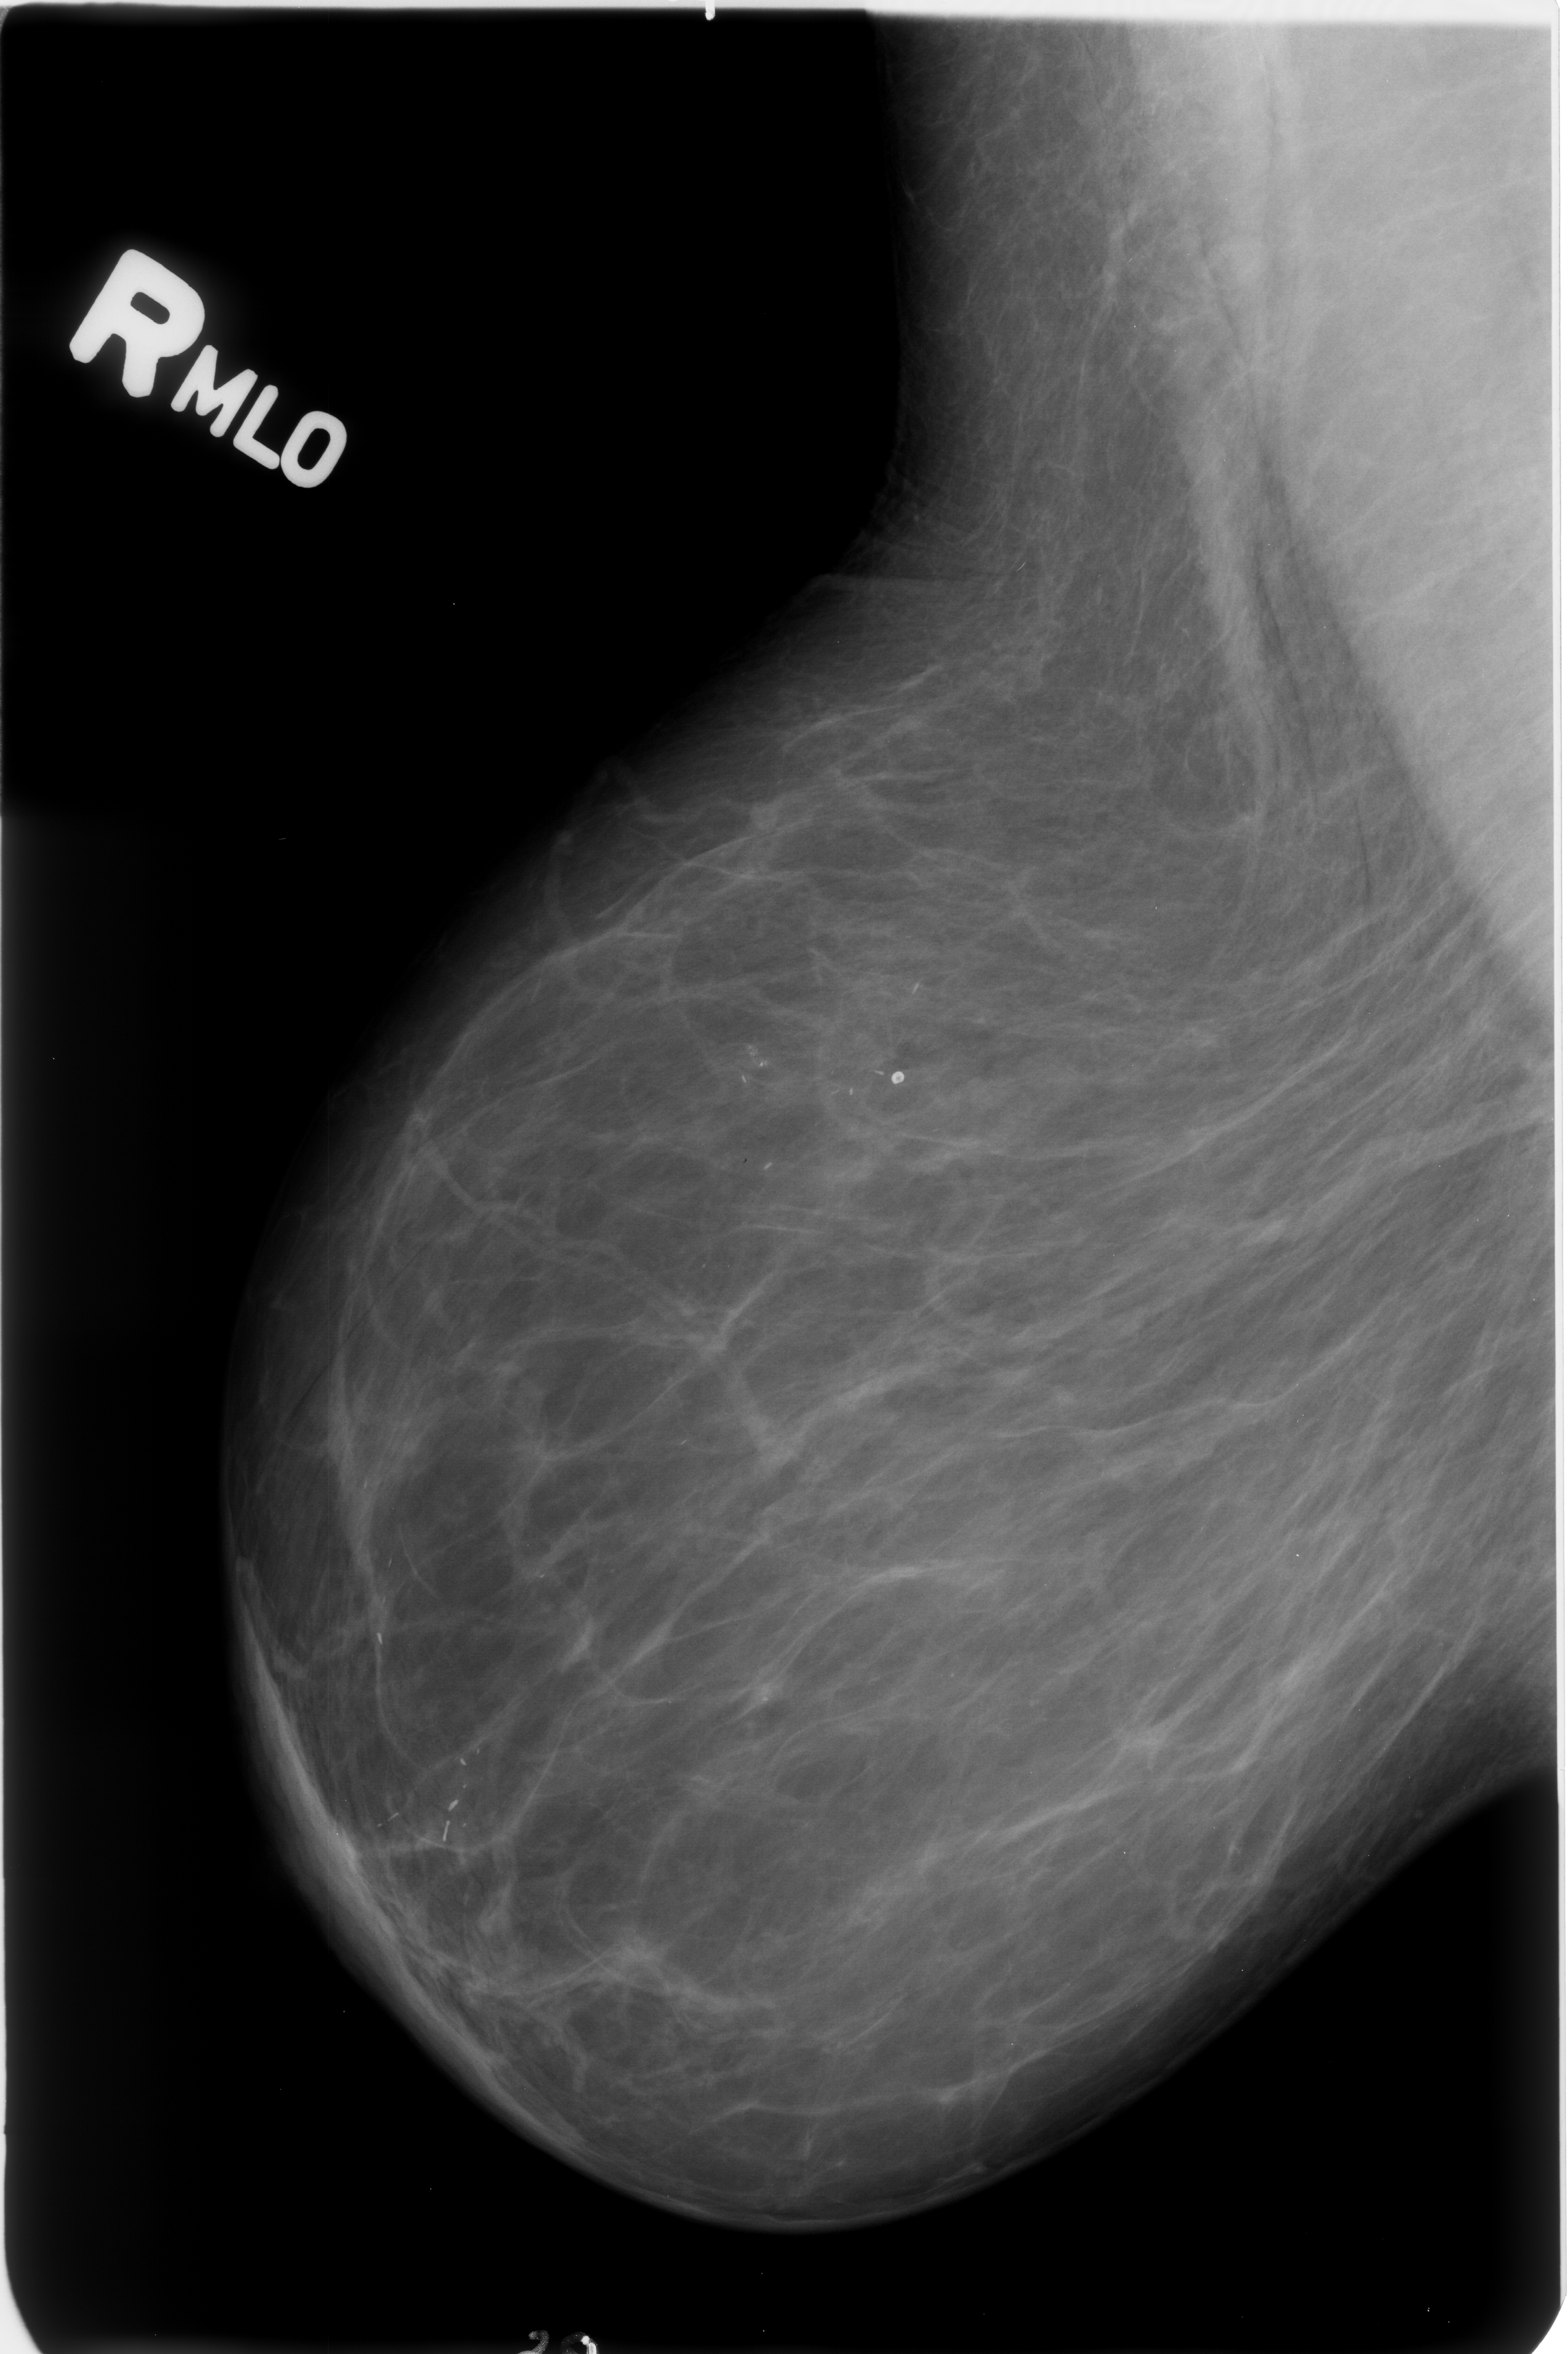
Digitized screen-film mammogram. Right breast. Mediolateral oblique (MLO) view. BI-RADS breast density category 1 (scale 1–4). 1568 × 2354 image matrix.
Expert-marked regions of interest on this film, with their recorded descriptors:
- Finding 1 of 5: calcifications, distribution regional; BI-RADS assessment category 2; subtlety rating 3 on a 1 (subtle) to 5 (obvious) scale; benign; no additional work-up was recommended (outcome (as recorded, no biopsy): benign without callback): bounding box [x1, y1, x2, y2] px = [349, 1547, 417, 1668]
- Finding 2 of 5: calcifications, distribution regional; BI-RADS assessment category 2; subtlety rating 3 on a 1 (subtle) to 5 (obvious) scale; benign; no additional work-up was recommended (outcome (as recorded, no biopsy): benign without callback): [358, 1802, 388, 1836]
- Finding 3 of 5: calcifications, distribution regional; BI-RADS assessment category 2; benign; no additional work-up was recommended (outcome (as recorded, no biopsy): benign without callback): [436, 1740, 495, 1865]
- Finding 4 of 5: calcifications, distribution regional; BI-RADS assessment category 2; subtlety rating 3 on a 1 (subtle) to 5 (obvious) scale; outcome (as recorded, no biopsy): benign without callback (not worked up further): [744, 1139, 787, 1178]
- Finding 5 of 5: calcifications, distribution regional; BI-RADS assessment category 2; outcome (as recorded, no biopsy): benign without callback (not worked up further): [893, 963, 943, 1013]